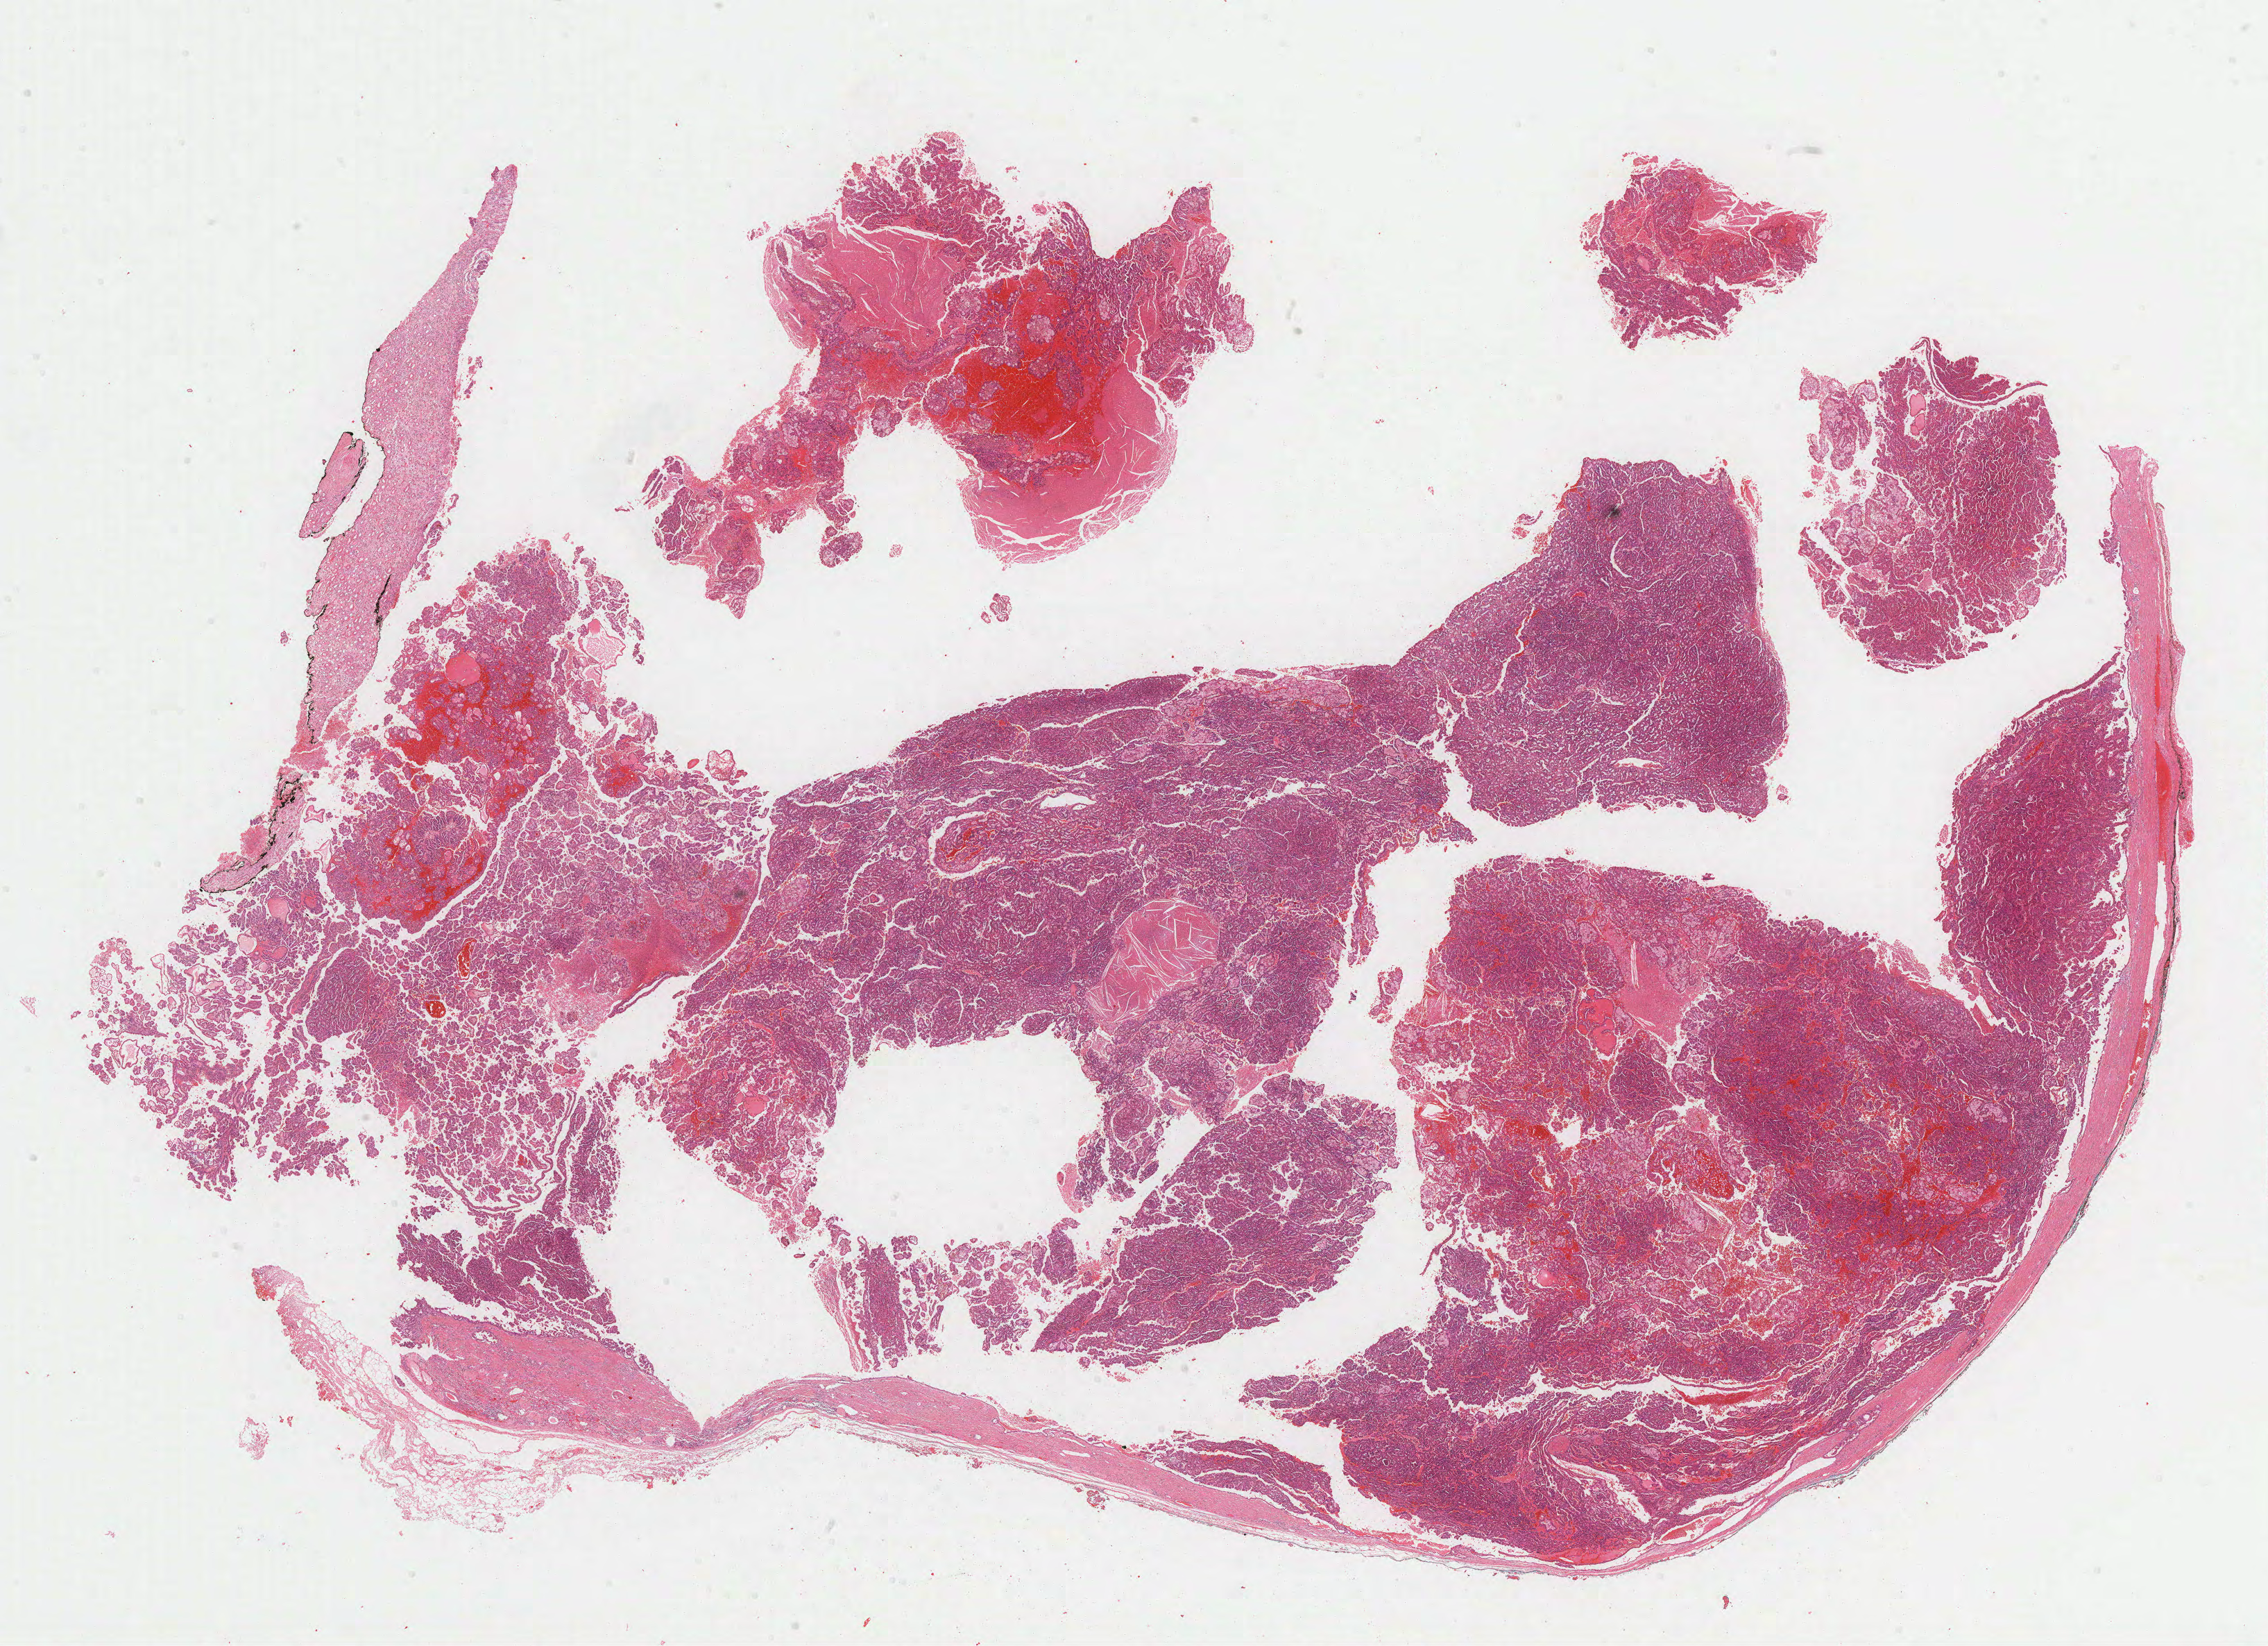
H&E whole-slide image, low-resolution overview of the scanned area, about 26.4 x 19.2 mm (from a 40x scan), formalin-fixed paraffin-embedded (FFPE) diagnostic section, sample: primary tumour, kidney. Patient: male, age at initial diagnosis 71 years.
TNM: T1a N0 MX. Laterality: left. AJCC pathologic stage: I (6th edition). Diagnosis: Papillary adenocarcinoma, NOS.